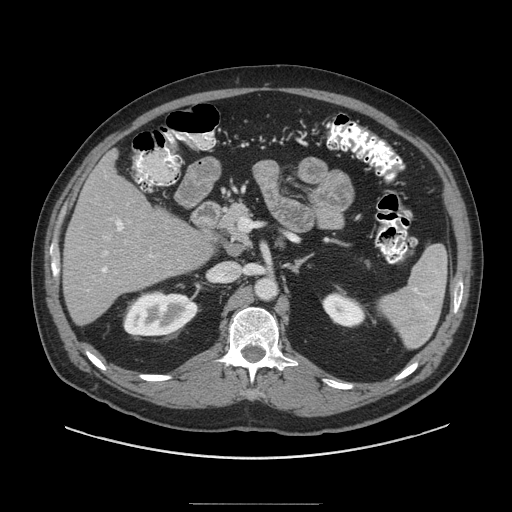
Contrast-enhanced abdominal CT (liver protocol), one axial slice. Position 47 of 91 along the scan axis. Reconstruction kernel STANDARD. 140 kVp. Soft-tissue window (W 400 / L 40 HU). 2.5 mm slice thickness. 512 × 512 image matrix, field of view 440 × 440 mm. From the clinical record (not read from this slice): diagnosis: hepatocellular carcinoma (patient treated with transarterial chemoembolisation; whether this scan precedes or follows treatment is not stated here); TNM stage (as recorded): Stage-I; Child-Pugh class: A; tumour differentiation: well differentiated; tumour nodularity: uninodular.
Structures marked on this image (semi-automatic segmentation, software-assisted and operator-edited):
- liver parenchyma outside the tumour (the mass and vessels are separate outlines, so this box may not span the whole liver): bounding box [x1, y1, x2, y2] px = [62, 150, 212, 324]
- liver vessels: [101, 218, 153, 273]